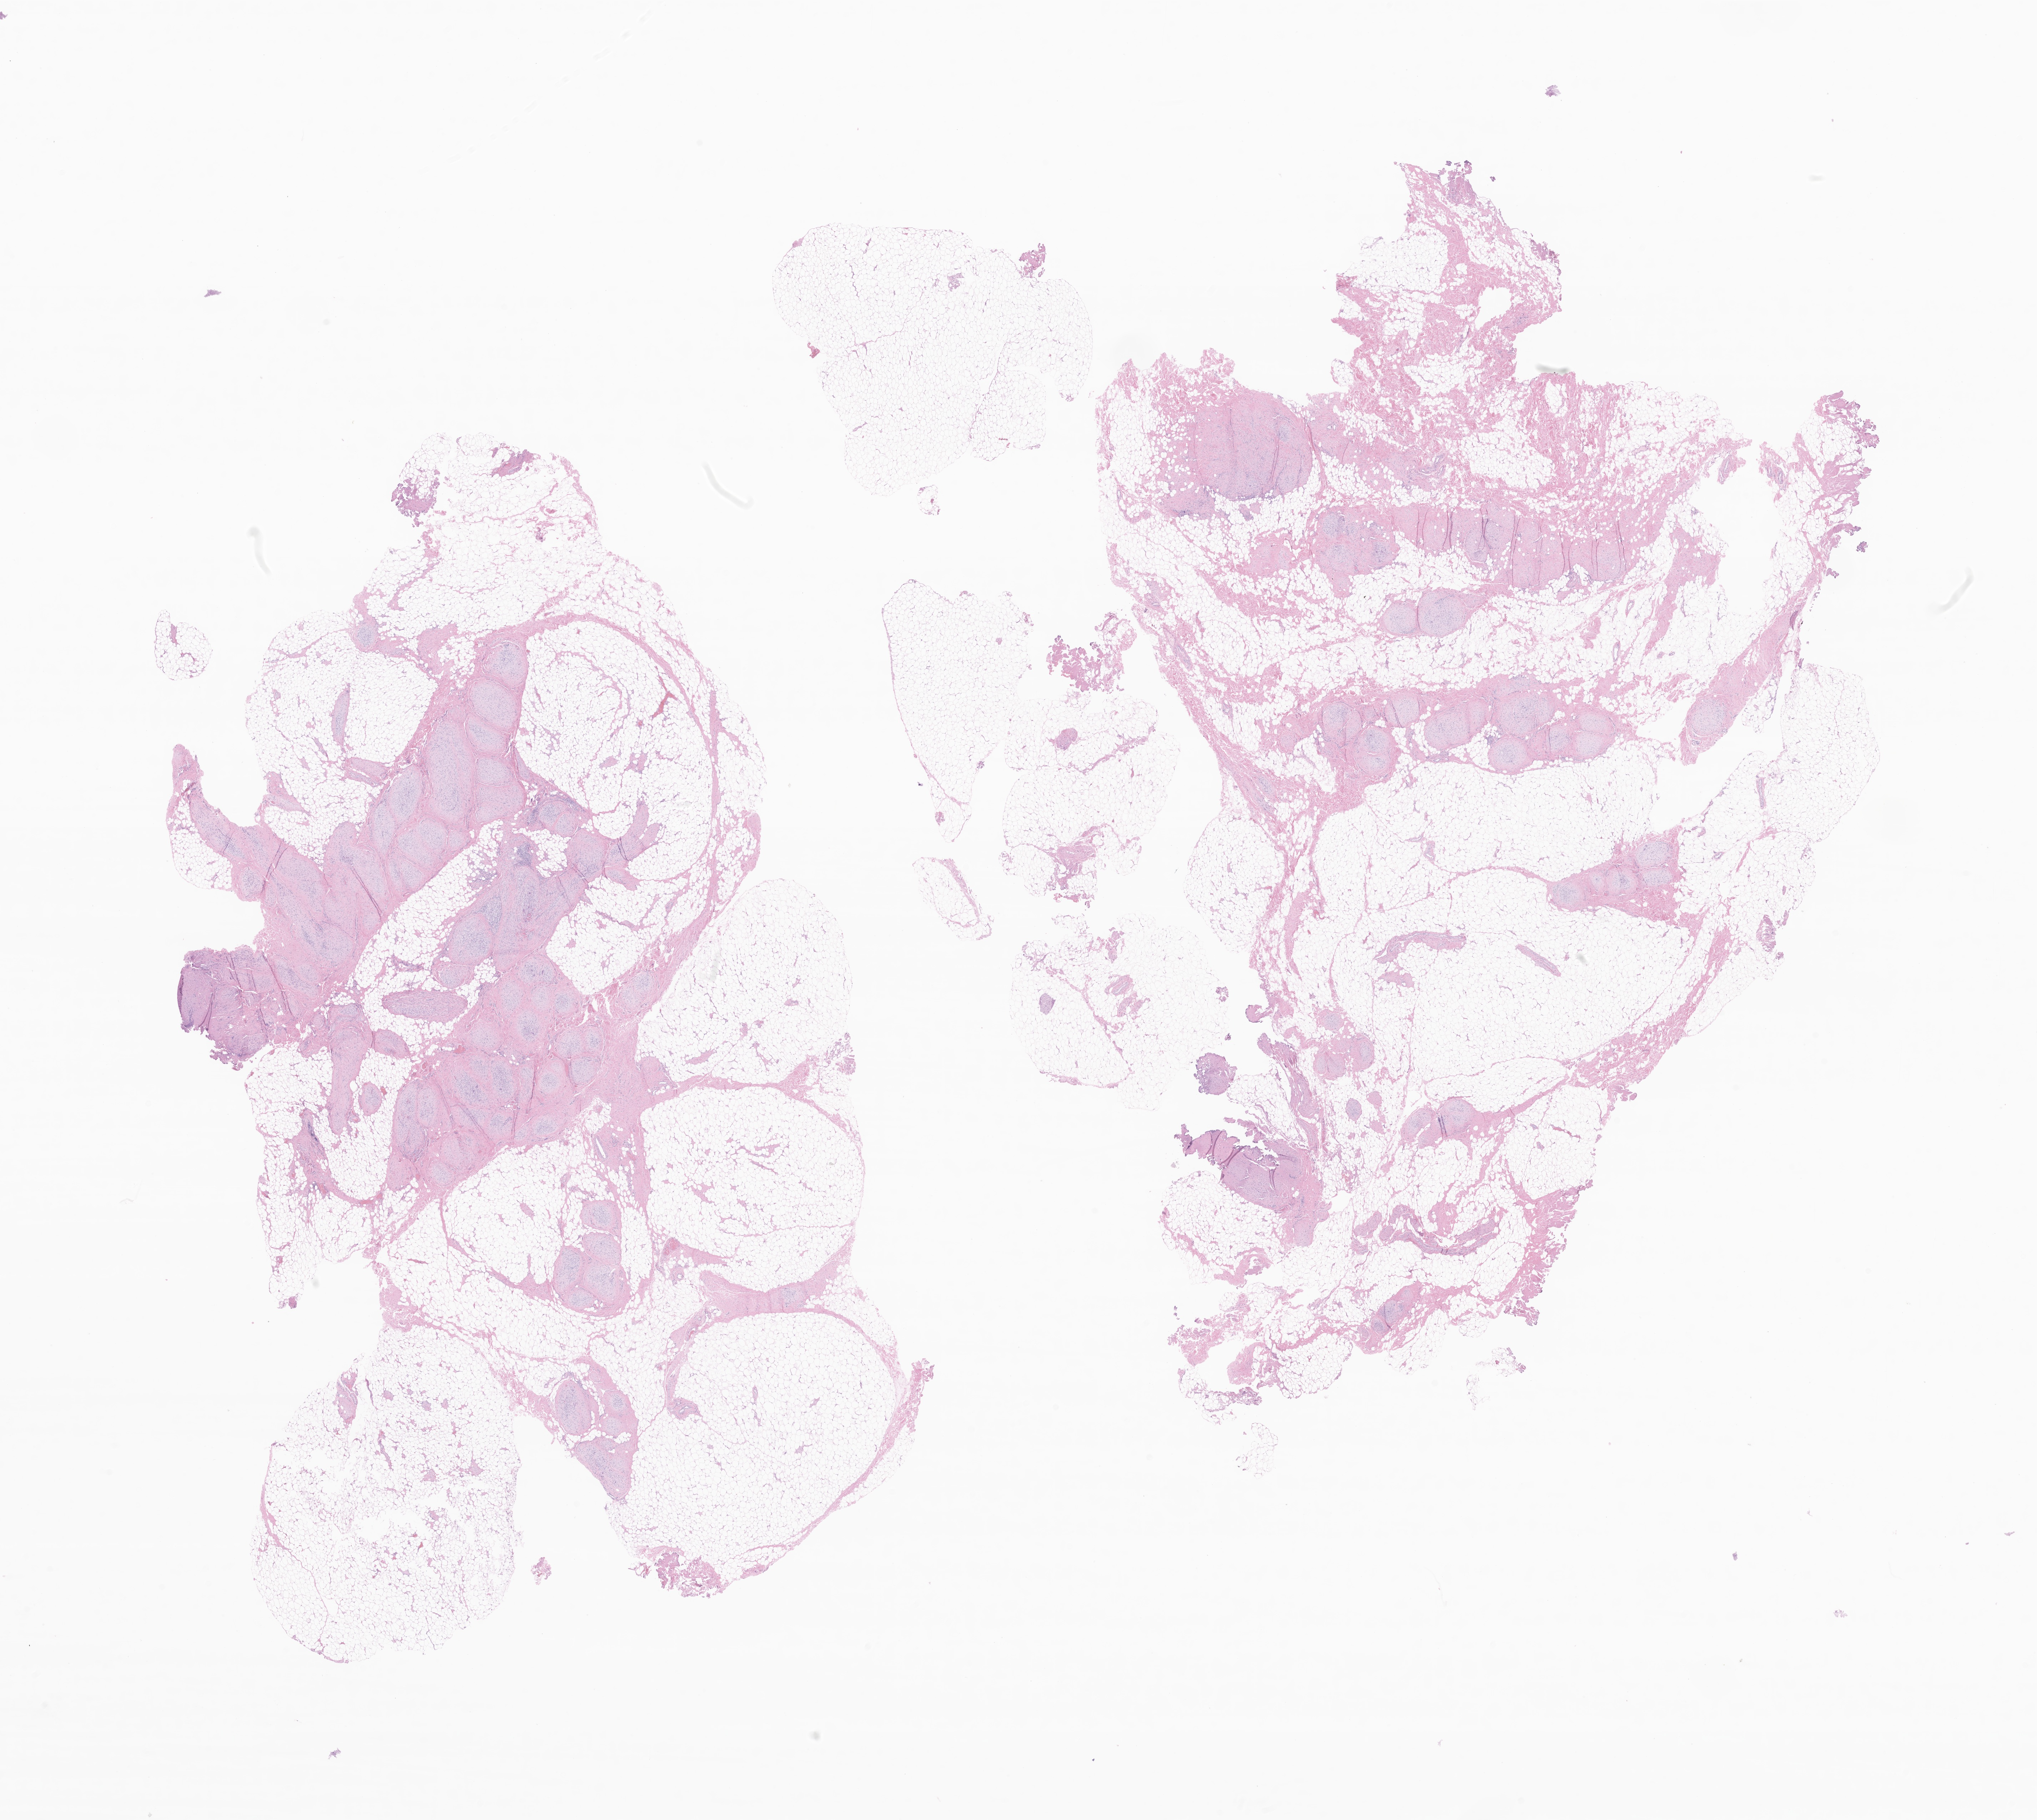
Whole-slide image, hematoxylin and eosin (H&E) stain of tumor tissue from the upper limb lymph node, whole scanned area (about 24.1 x 21.5 mm) shown as a low-resolution overview; formalin-fixed paraffin-embedded section. Patient male; age 201 months (16 years 9 months).
Diagnosis (ICD-O-3 morphology term): Plexiform fibrohistiocytic tumor.